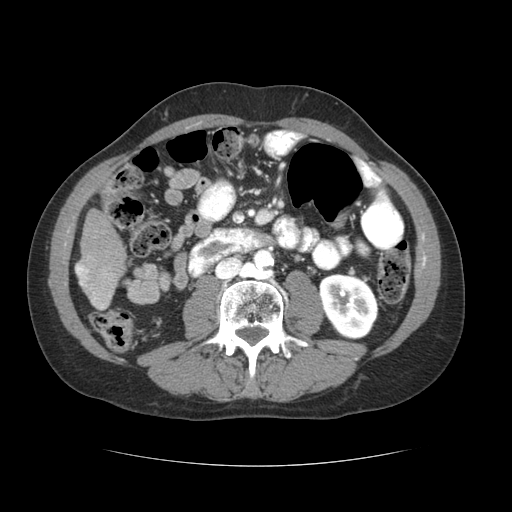
Contrast-enhanced abdominal CT (liver protocol), one axial slice; slice 10 of 69 in the series (ordered by position); soft-tissue window (W 400 / L 40 HU); 2.5 mm slice thickness; 512 × 512 image matrix, field of view 360 × 360 mm. Case-level facts recorded for this patient, not image findings: diagnosis: hepatocellular carcinoma (patient treated with transarterial chemoembolisation; whether this scan precedes or follows treatment is not stated here); TNM stage (as recorded): Stage-II; Child-Pugh class: B; tumour size: 2.6 cm.
Outlined on this slice (semi-automatic segmentation, software-assisted and operator-edited):
- liver parenchyma outside the tumour (the mass and vessels are separate outlines, so this box may not span the whole liver): box from (x=74, y=210) to (x=126, y=310) px
- liver vessels: (x=76, y=264)–(x=111, y=308)